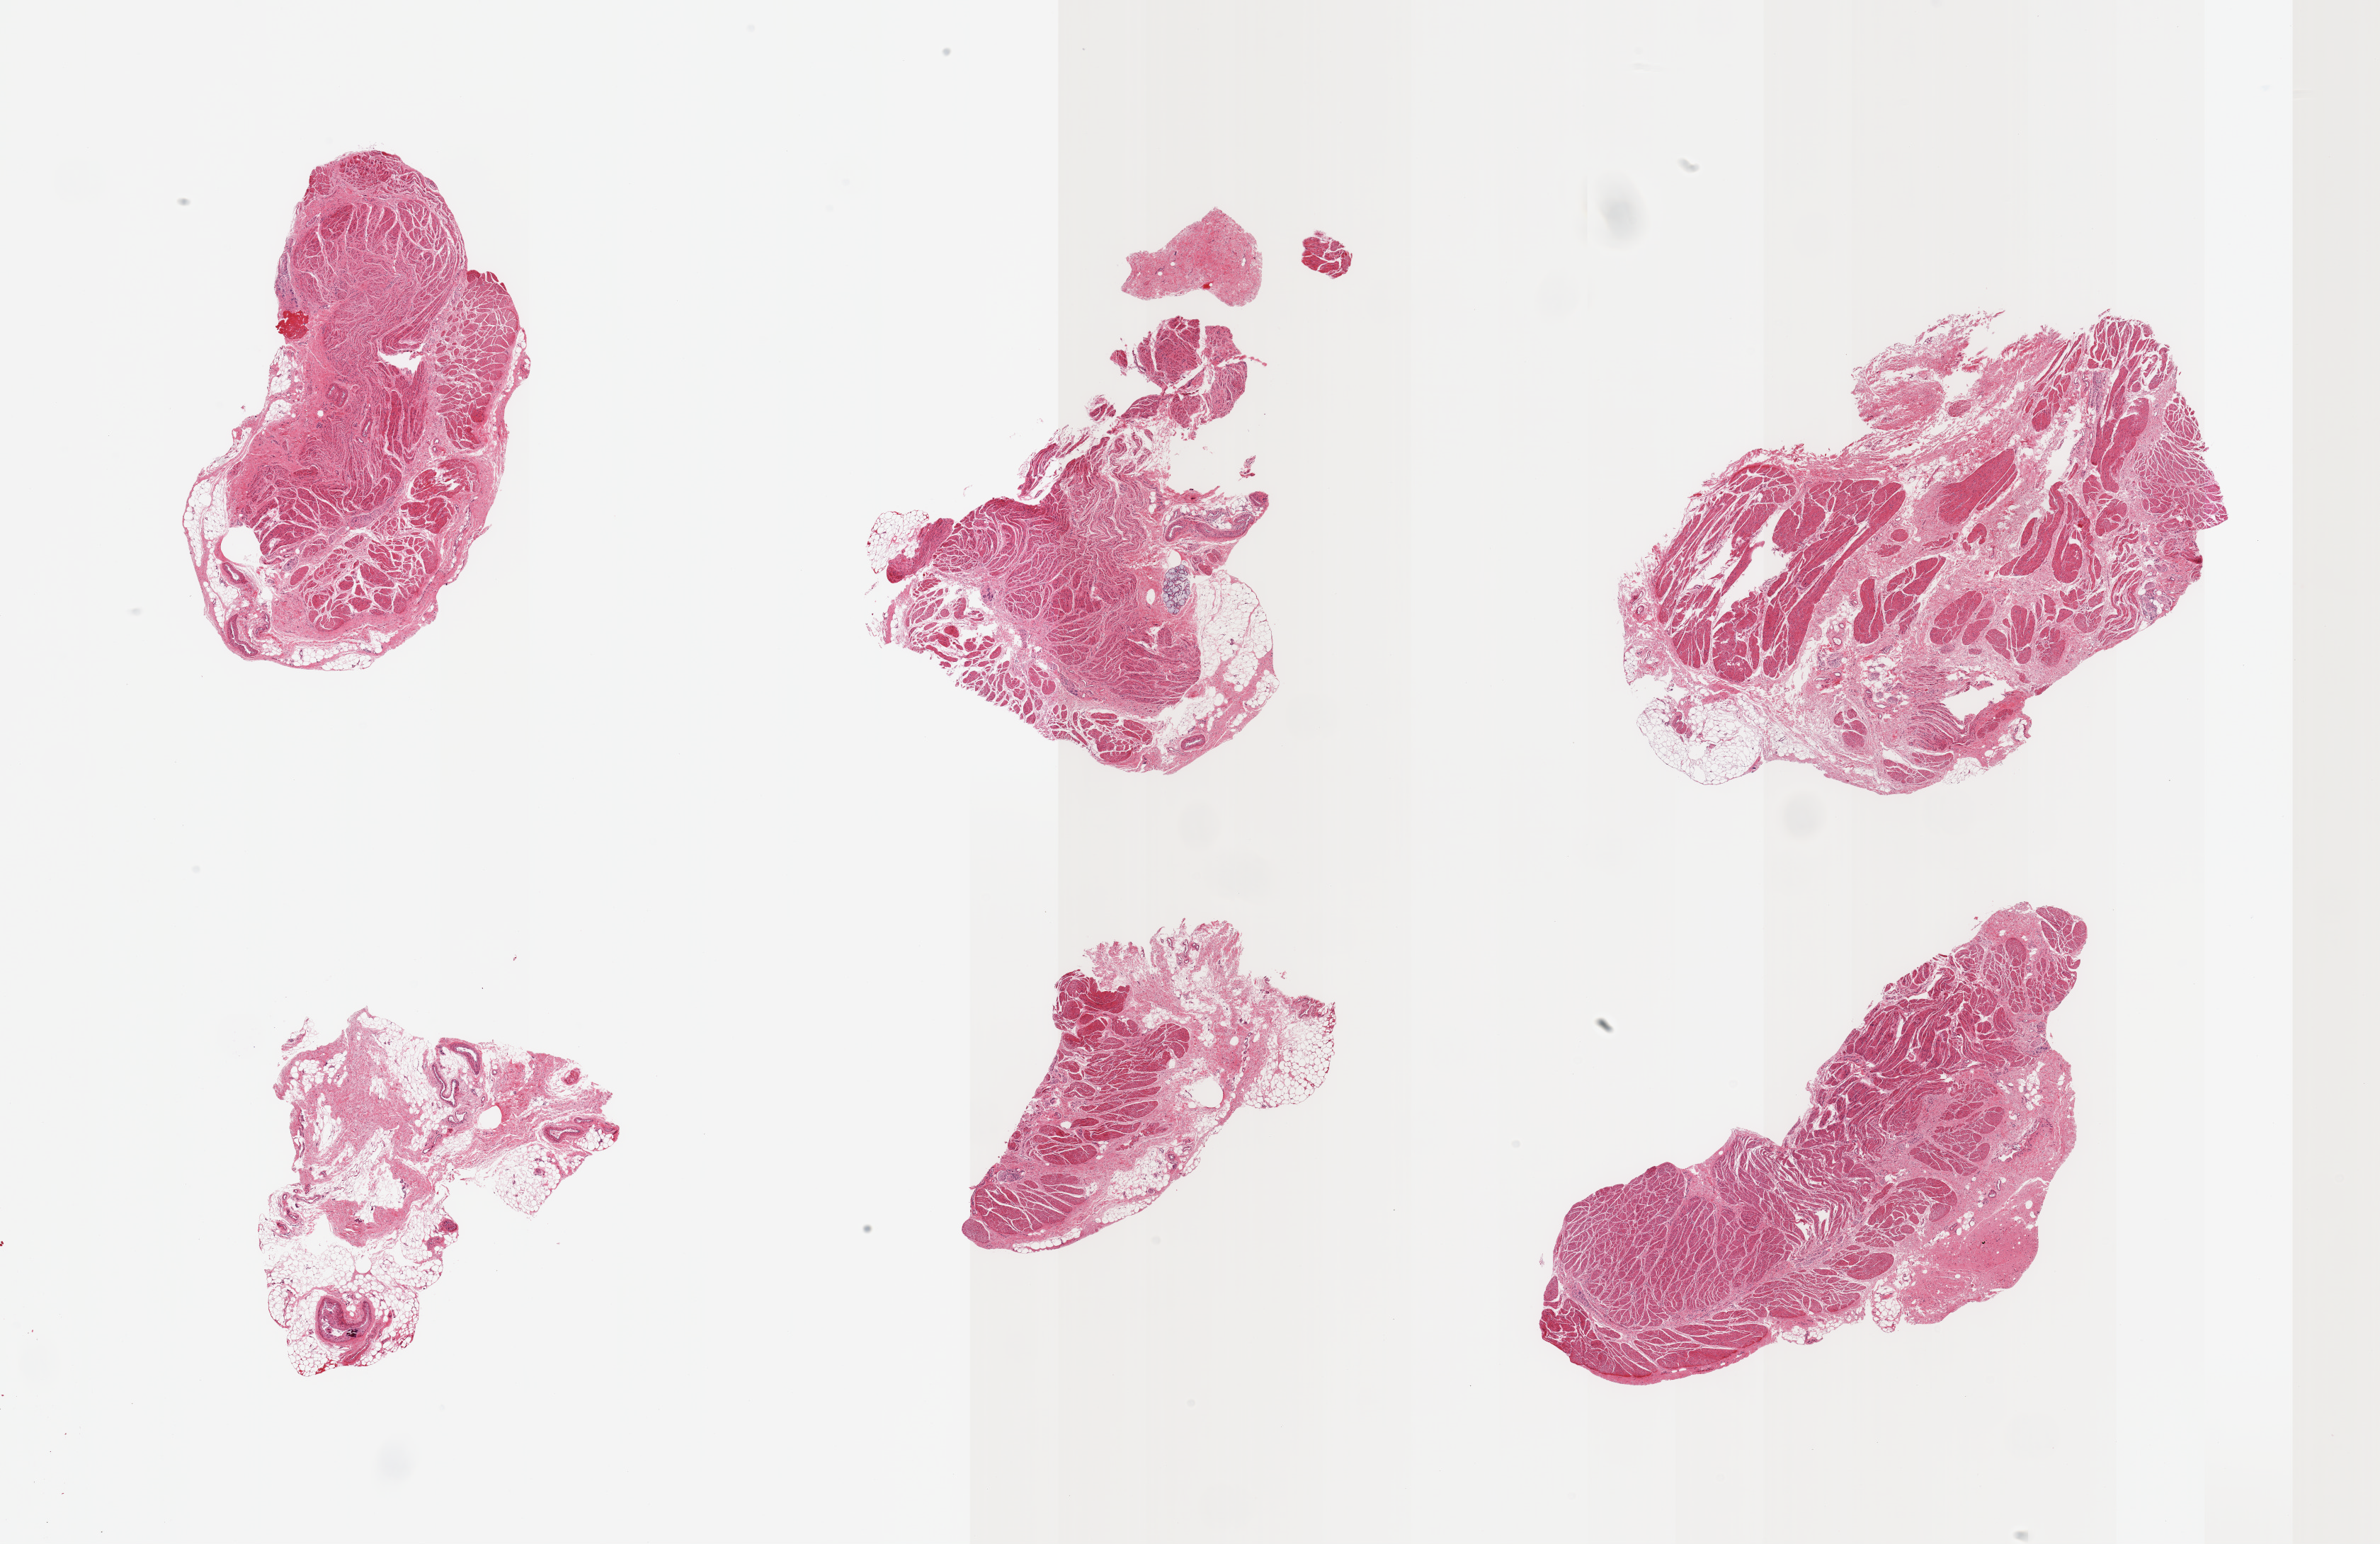
Whole-slide image, haematoxylin and eosin stain — shown as a low-resolution overview of the whole scanned area (about 26.6 x 17.2 mm); PAXgene-fixed paraffin-embedded (PFPE) section; target tissue: gastroesophageal junction; tissue donor sample. Male donor.
Pathologist's review note for this sample: 6 pieces ~60% target muscularis, contaminant fat/fascia, mucus glands present.